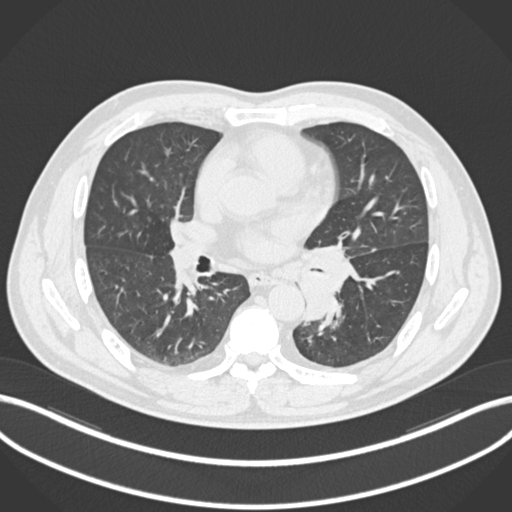
Chest CT, one axial slice; slice 116 of 223 in the series (ordered by position); 120 kVp; lung window (W 1500 / L -600 HU); 1 mm slice thickness; 512 × 512 image matrix, field of view 400 × 400 mm. Patient: male, 50 years. From the clinical record (not read from this slice): clinical TNM (as recorded): T2a N3 M0.
Outlined on this slice (bounding box drawn by a radiologist):
- lung tumour (recorded histology: squamous cell carcinoma): box from (x=293, y=244) to (x=354, y=326) px